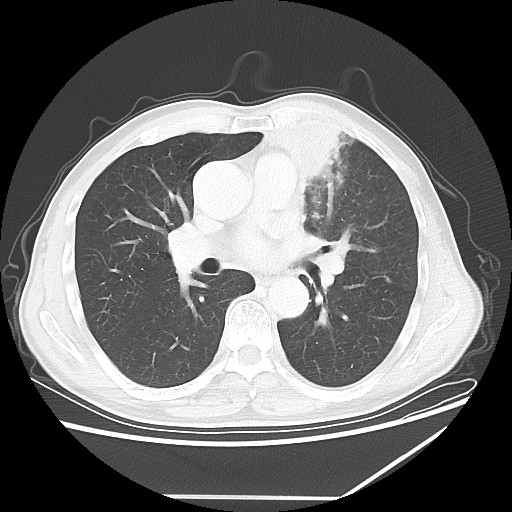
Chest CT, one axial slice; slice 34 of 64 in the series (ordered by position); 100 kVp; lung window (W 1500 / L -600 HU); 5 mm slice thickness; 512 × 512 image matrix. Patient: male, 64 years. From the clinical record (not read from this slice): clinical TNM (as recorded): T1c N1 M1.
Annotated regions visible in this slice (bounding box drawn by a radiologist):
- lung tumour (recorded histology: squamous cell carcinoma): bounding box <265,105,369,195> (left, top, right, bottom; pixels)